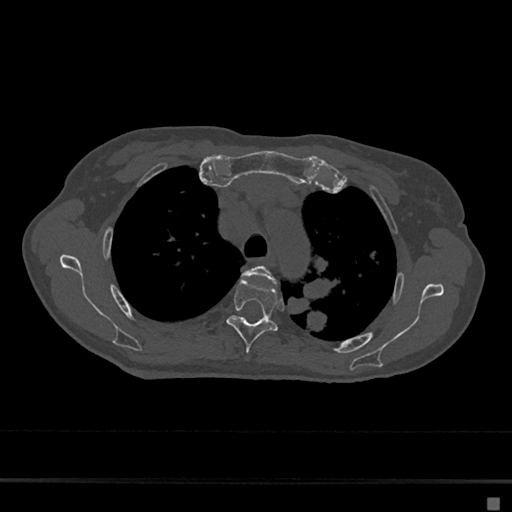
CT including the spine, one axial slice; position 502 of 797 along the scan axis; 120 kVp; bone window (W 1800 / L 400 HU); 0.5 mm slice thickness; 512 × 512 image matrix. Female patient, age 68 years. From the clinical record (not read from this slice): primary cancer: renal.
Annotated regions visible in this slice (semi-automatically segmented with operator editing):
- T3 vertebra: bounding box [x1, y1, x2, y2] px = [243, 265, 276, 283]
- T4 vertebra: [226, 279, 278, 353]